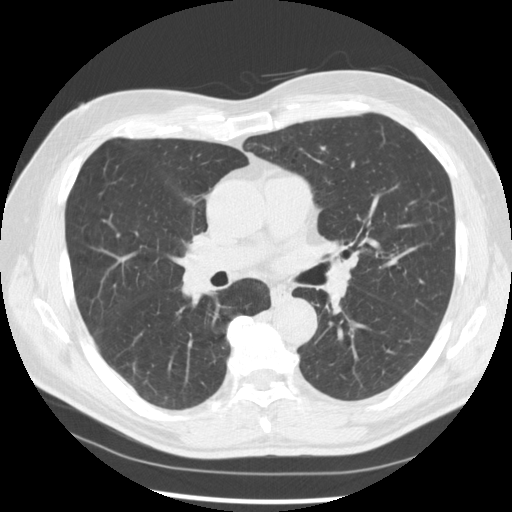
Low-dose screening chest CT, one axial slice. Slice 158 of 277 in the series (ordered by position). Reconstruction kernel STANDARD. 120 kVp. Lung window (W 1500 / L -600 HU). 2.5 mm slice thickness. 512 × 512 image matrix, field of view 365 × 365 mm.
Annotated regions visible in this slice (manually delineated by an expert):
- lesion 1 (tumor, middle lobe of right lung): bounding box <181,269,210,300> (left, top, right, bottom; pixels)